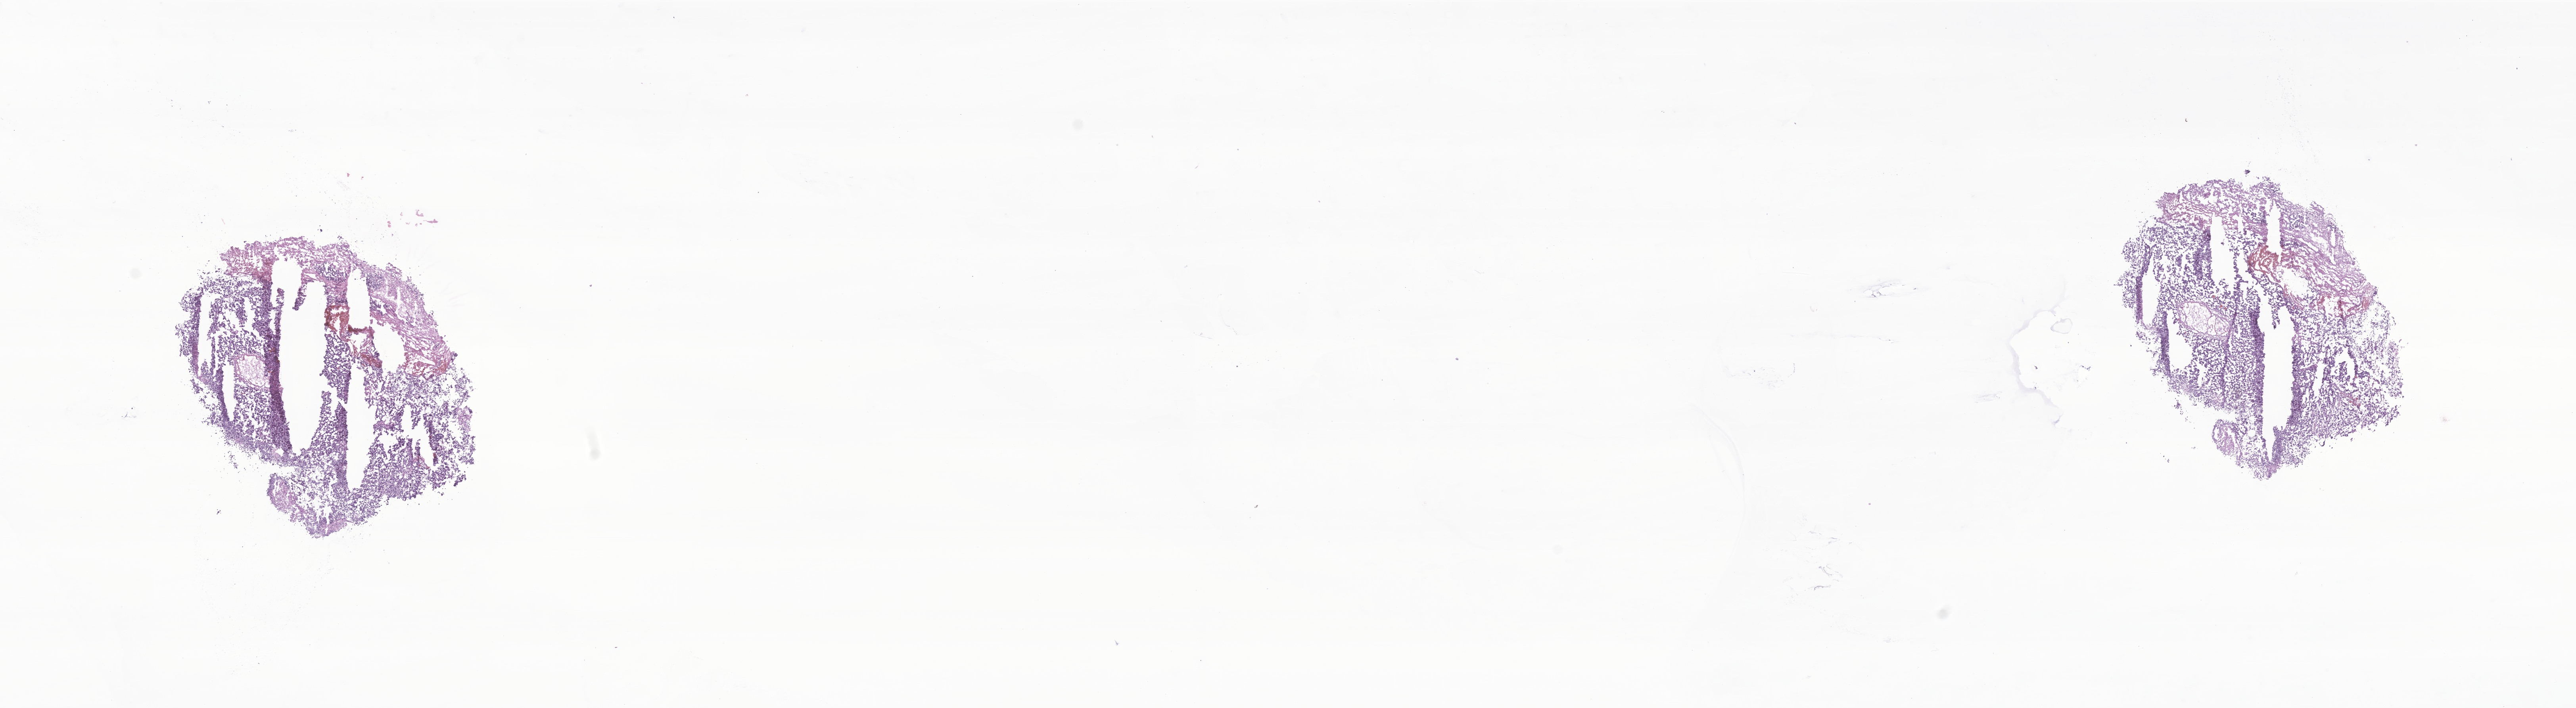
Digitized hematoxylin and eosin (H&E)-stained section of tumor tissue from the cerebellum — low-resolution overview of the scanned area, about 27.4 x 7.5 mm; cryosection (OCT / tissue freezing medium). Female patient, age 902 days.
Recorded diagnosis: Neoplasm, malignant.